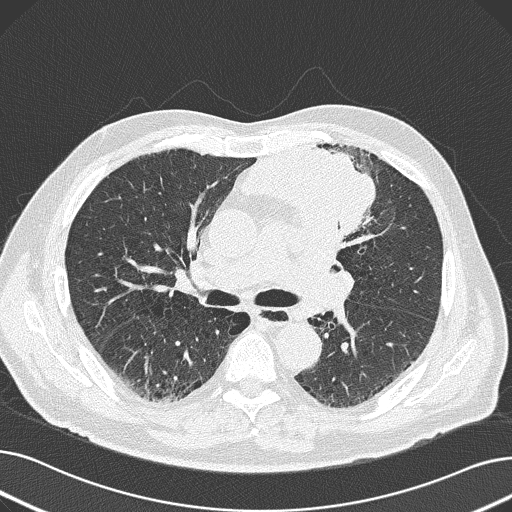
Low-dose screening chest CT, axial slice, baseline annual screen, lung window (W 1500 / L -600 HU), 2 mm slice thickness, lung (sharp) reconstruction kernel (B50f), slice 75 of 165 in the series, 512 × 512 image matrix. Male, age 69 years at enrolment. Former smoker at enrolment.
Expert reader's lesion annotation, bounding box <236,133,385,250> (left, top, right, bottom; pixels). Reader record for this screening exam (exam-level; its link to the box is not recorded): non-calcified nodule or mass ≥4 mm, left upper lobe, 6 × 10 mm, spiculated (stellate) margins, soft tissue attenuation. Lung cancer was diagnosed 20 days after this screen: non-small cell carcinoma, left upper lobe, poorly differentiated (G3), stage IB (AJCC 6th edition), 100 mm at pathology.